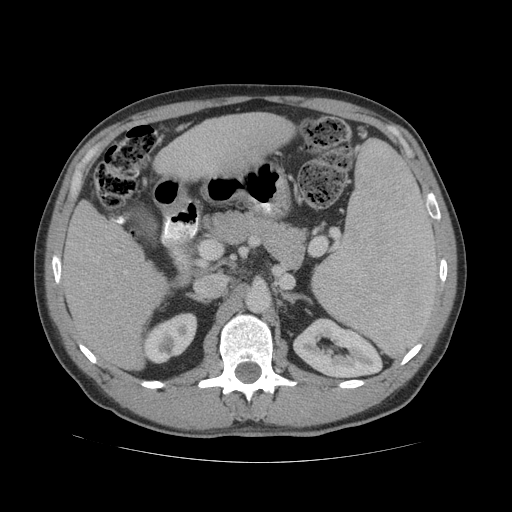
Contrast-enhanced abdominal CT (liver protocol), one axial slice; position 28 of 81 along the scan axis; reconstruction kernel STANDARD; 140 kVp; soft-tissue window (W 400 / L 40 HU); 2.5 mm slice thickness; 512 × 512 image matrix, field of view 400 × 400 mm. From the clinical record (not read from this slice): diagnosis: hepatocellular carcinoma (patient treated with transarterial chemoembolisation; whether this scan precedes or follows treatment is not stated here); TNM stage (as recorded): Stage-IVB; Child-Pugh class: B; tumour differentiation: well differentiated; tumour nodularity: multinodular.
Outlined on this slice (semi-automatically segmented with operator editing):
- liver parenchyma outside the tumour (the mass and vessels are separate outlines, so this box may not span the whole liver): bounding box (x1, y1, x2, y2) in pixels: (60, 112, 294, 370)